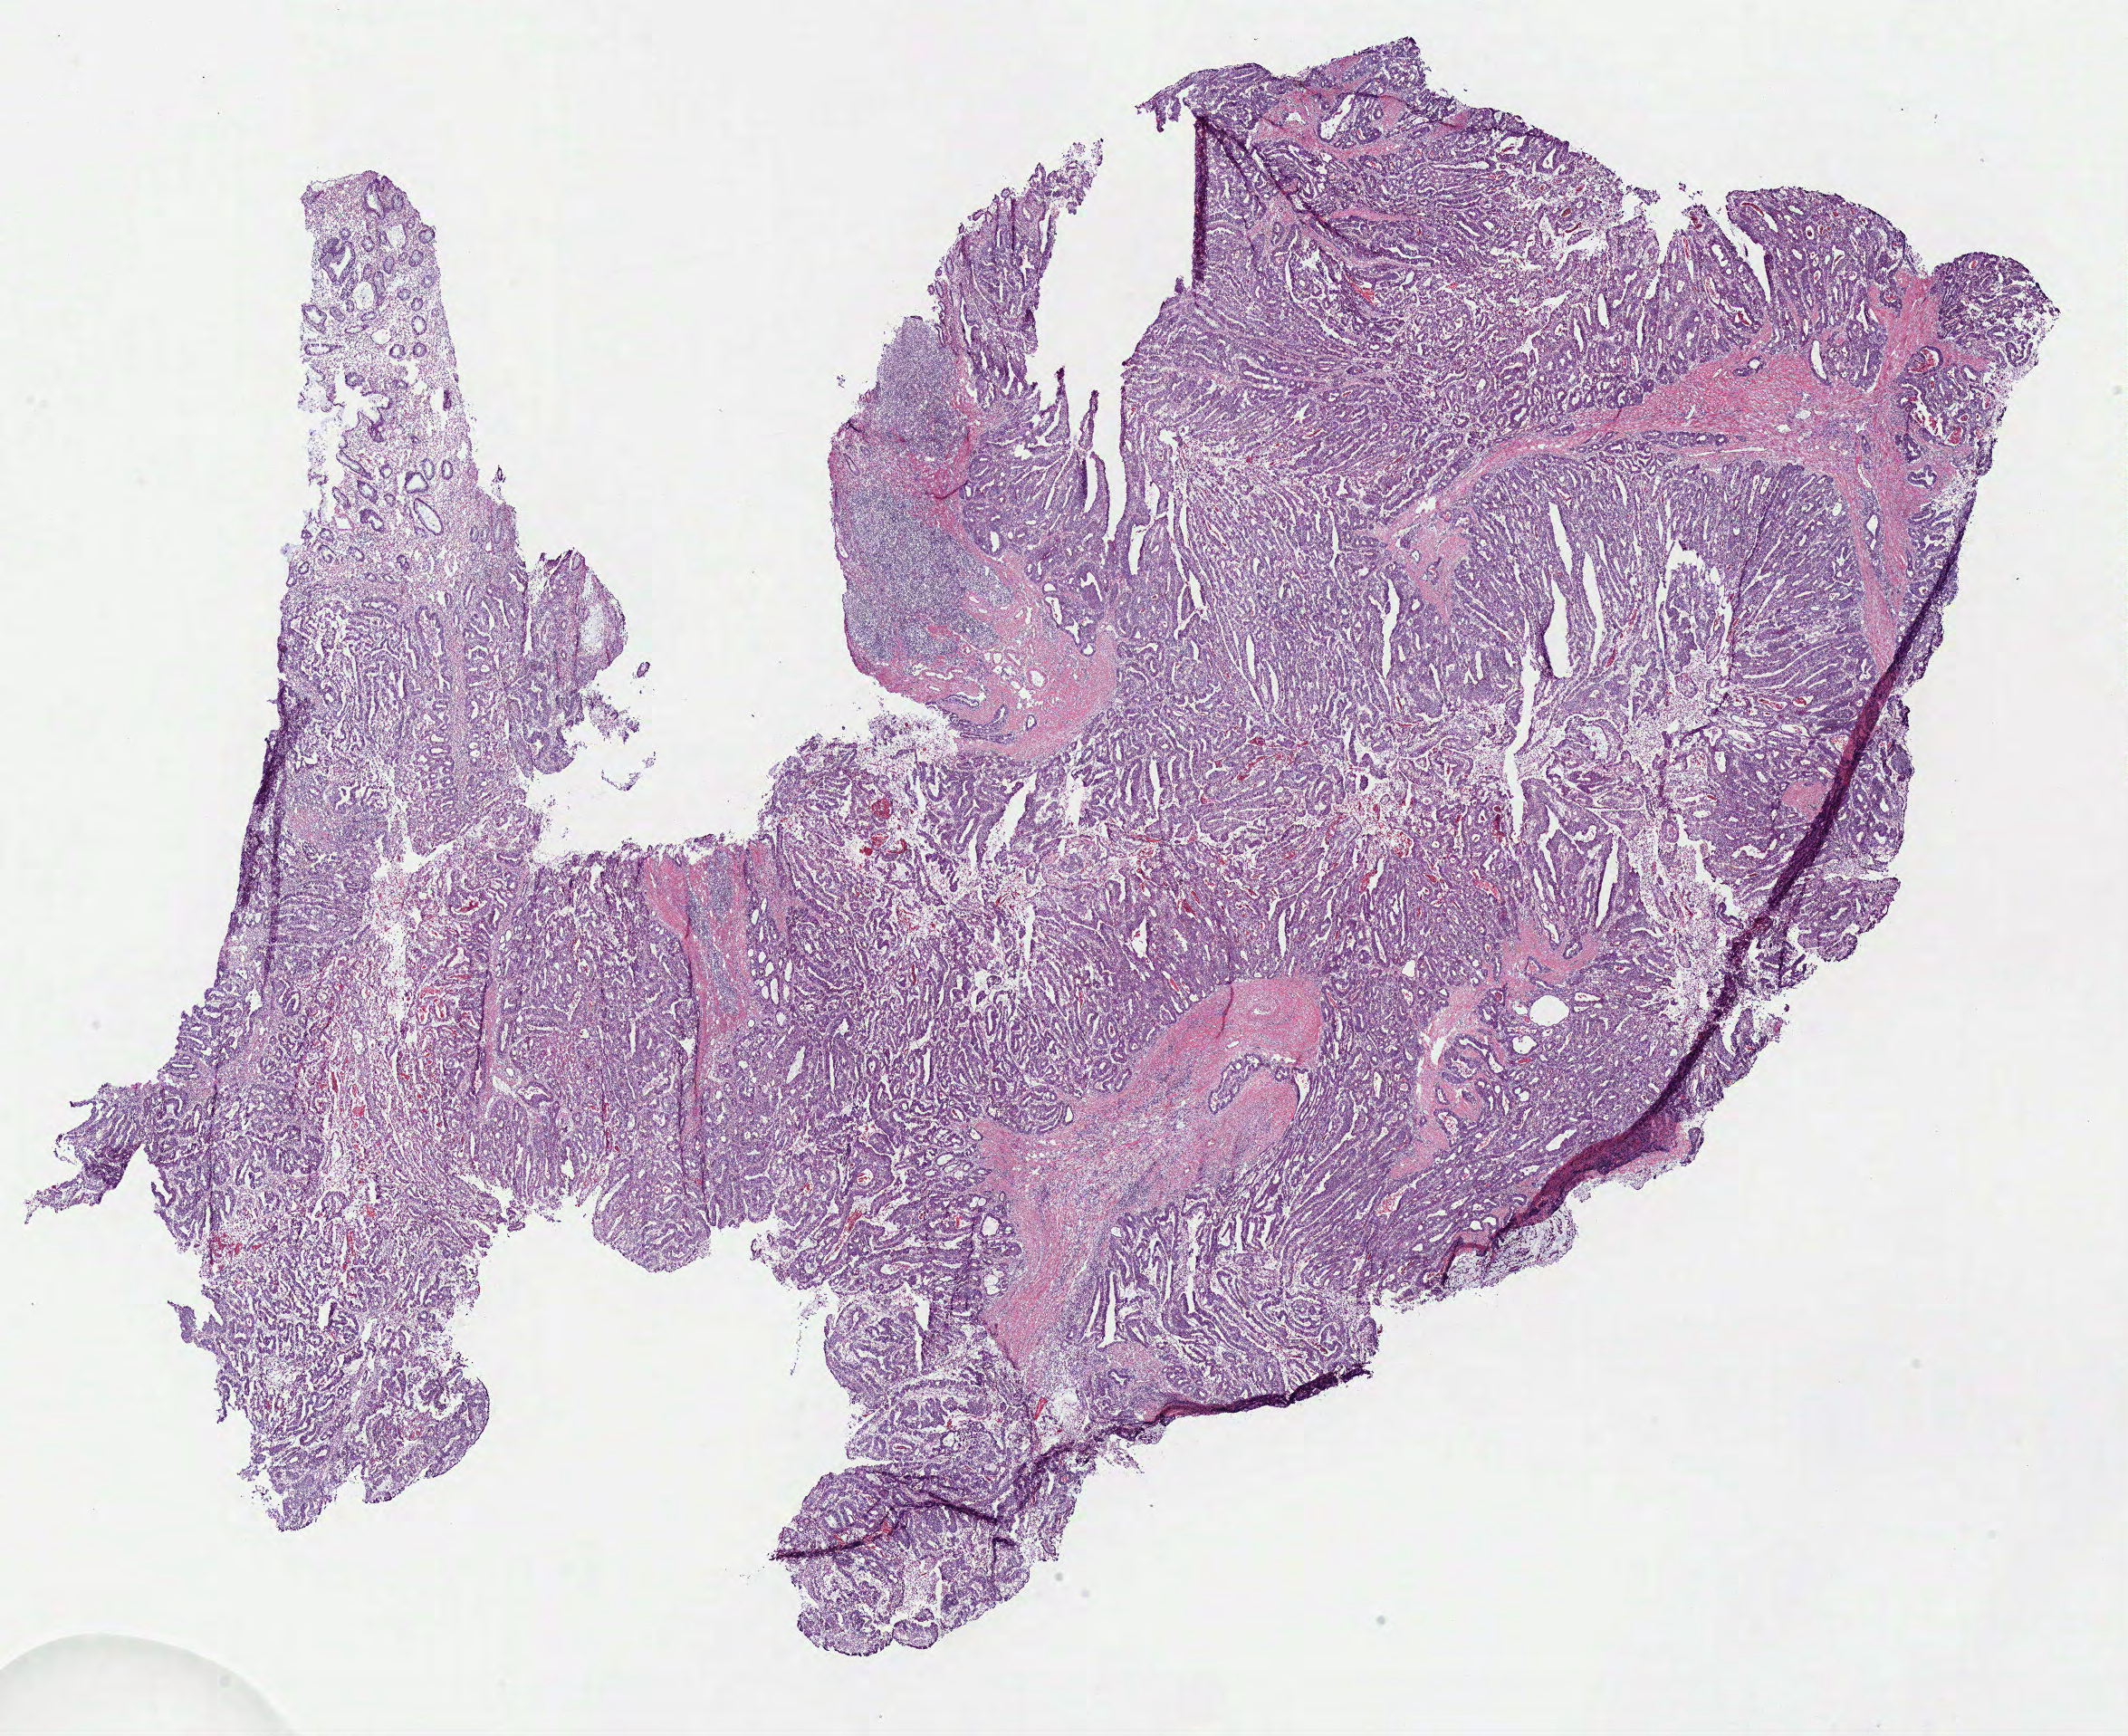
Digitized H&E-stained tissue section (whole slide) — whole scanned area (about 18.5 x 15.1 mm, acquisition: 40x scan) shown as a low-resolution overview, frozen section from the bottom of the tissue portion, sample: primary tumour, colon. Male, age 60 years at initial diagnosis. Pathologist review of this section (percent, as recorded): tumour cells 90%, tumour nuclei 80%, normal cells 5%, stromal cells 4%, necrosis 1%. Infiltration values recorded for this section: lymphocyte infiltration 10%, monocyte infiltration 2%, neutrophil infiltration 4%.
Histologic diagnosis: Adenocarcinoma, NOS. AJCC pathologic stage: I (7th edition). Lymph nodes positive (case pathology): 0 of 33 examined.